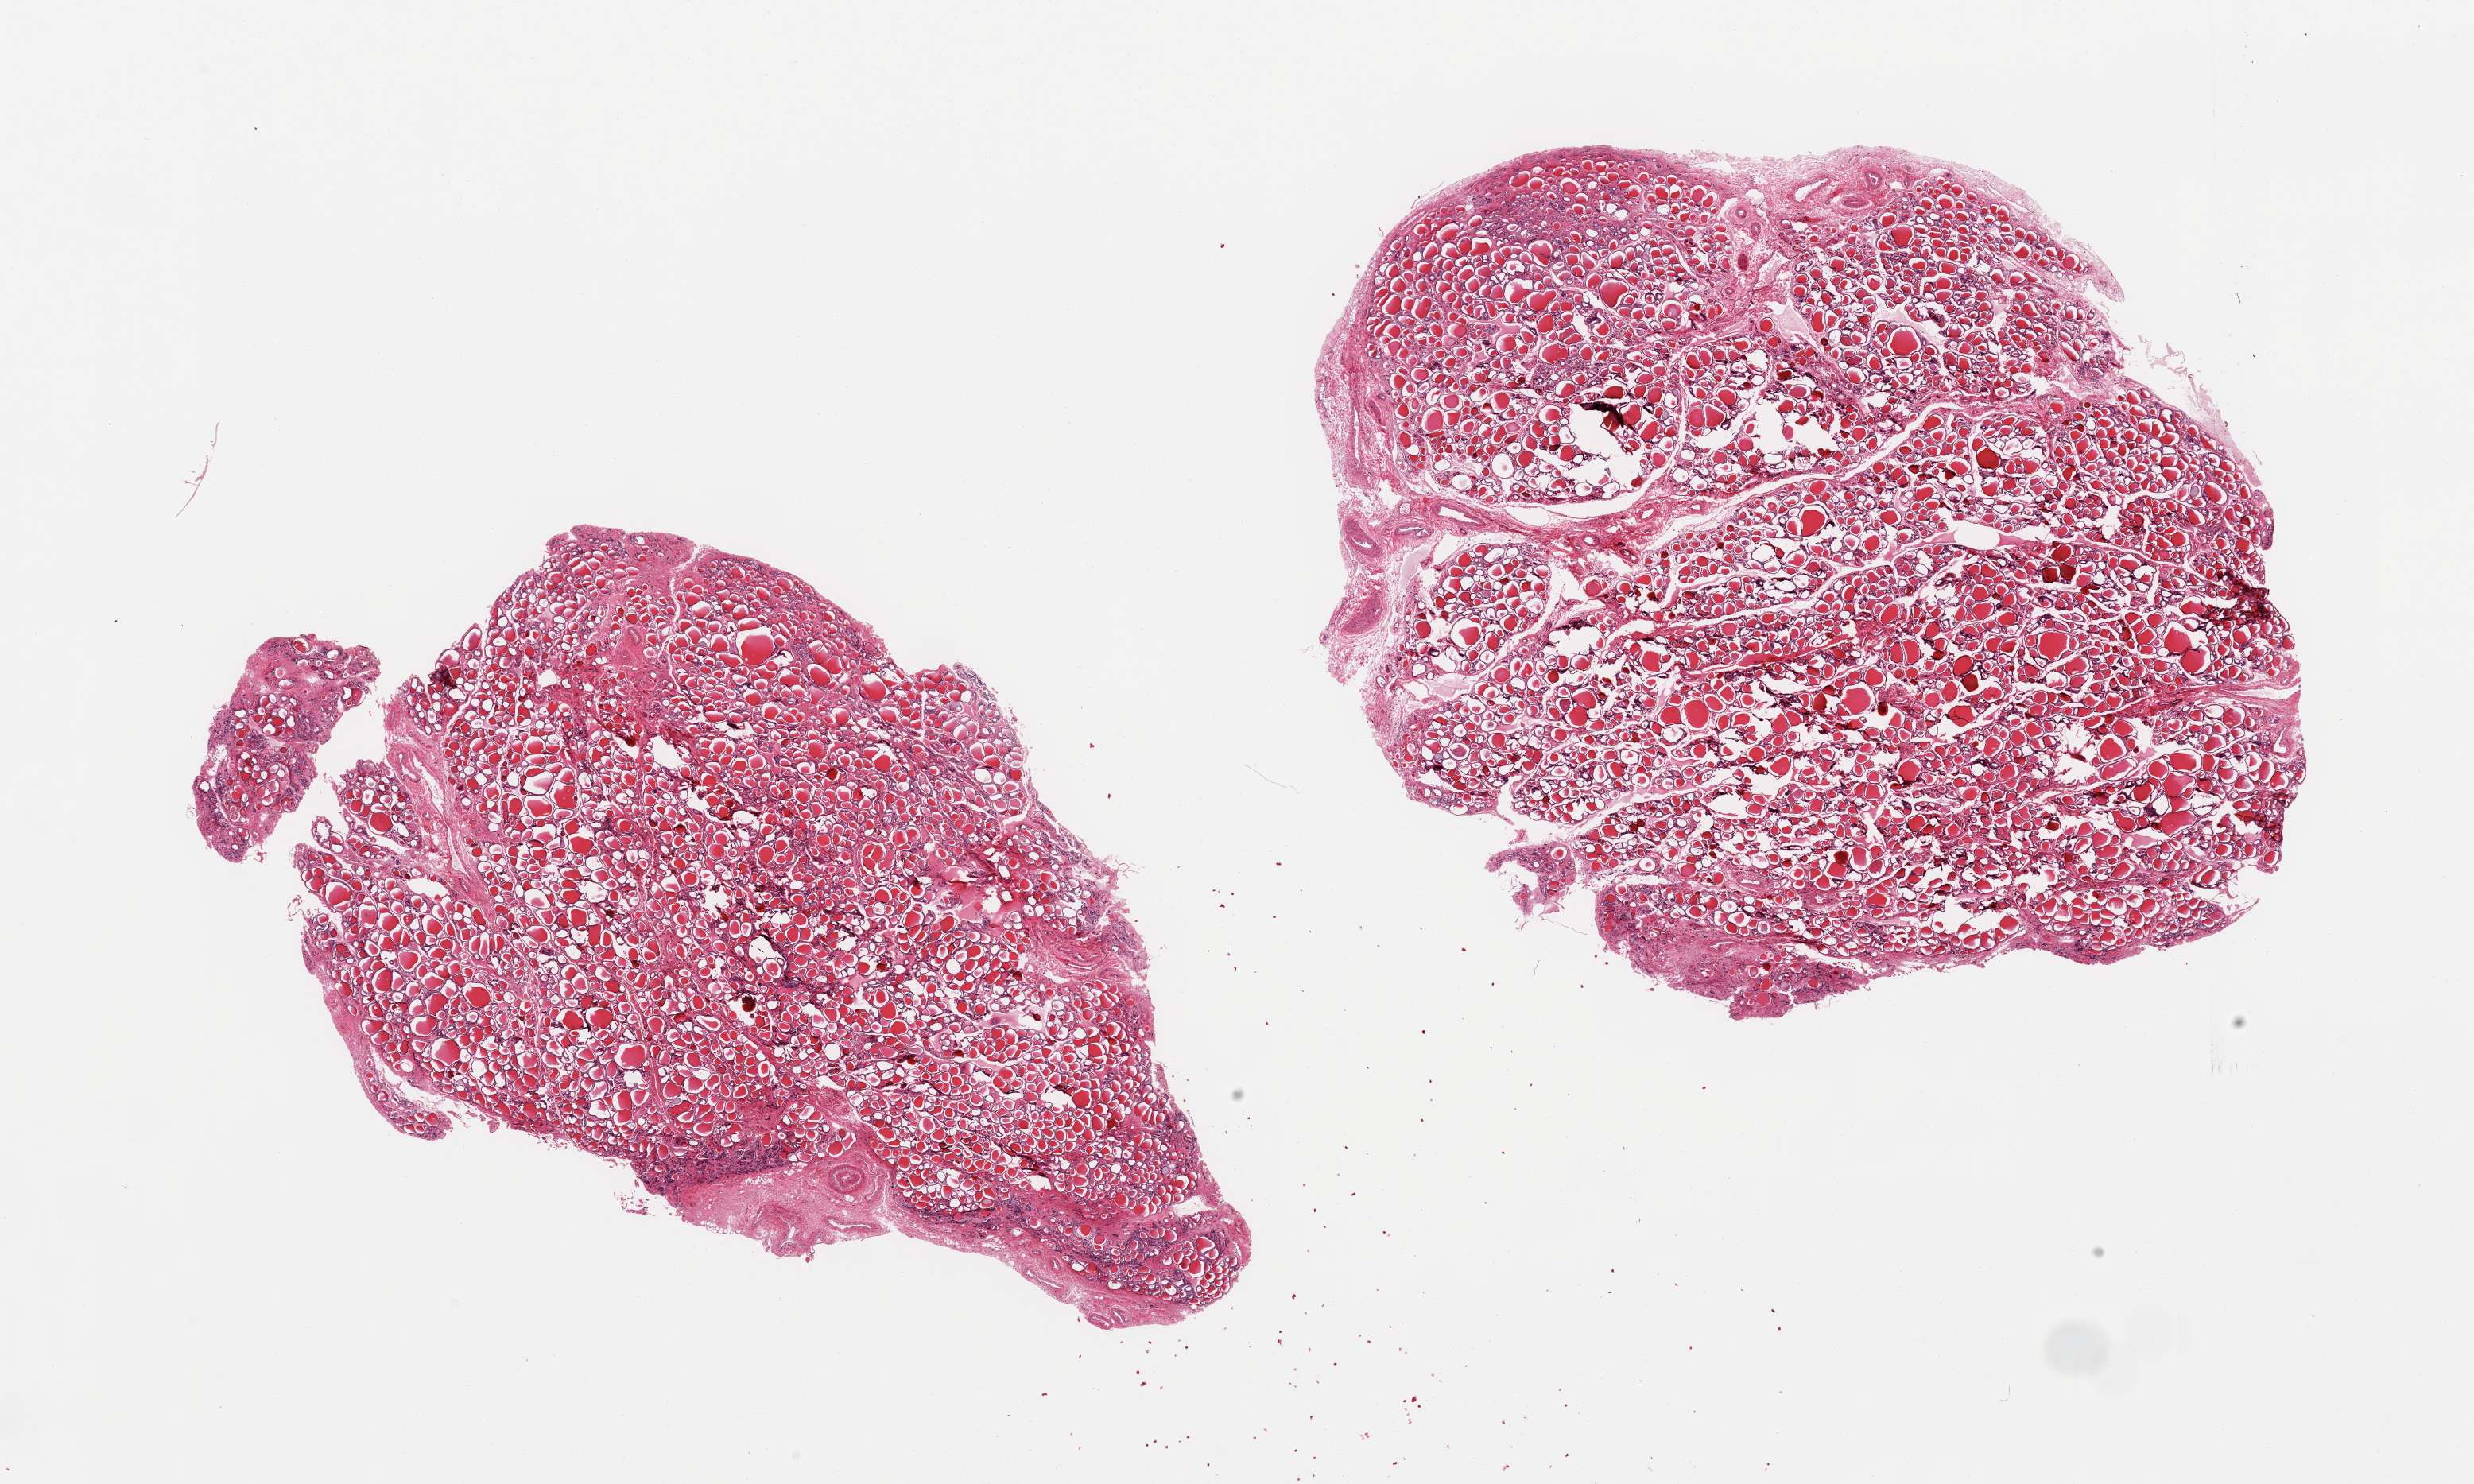
Whole-slide image, H&E stain, low-resolution overview of the scanned area, about 24.6 x 14.8 mm. PAXgene-fixed paraffin-embedded (PFPE) section. Sampled site (target tissue): thyroid. Donor tissue sample.
- reviewer comment on this tissue sample: 2 pieces; small foci of scarring